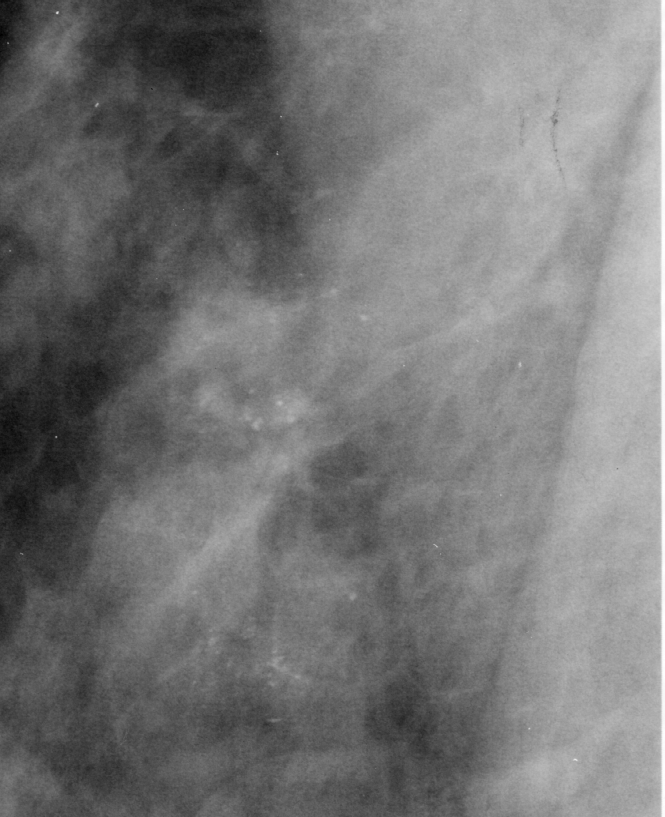
Crop from a digitized film mammogram around one marked abnormality, right breast, MLO view, BI-RADS breast density category 3 (scale 1–4).
Marked abnormality: calcifications, morphology punctate / pleomorphic, distribution clustered; BI-RADS assessment category 4; pathology (as recorded): malignant.